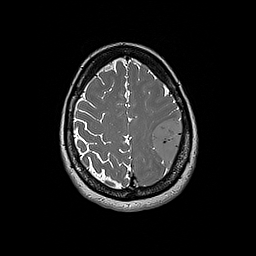
Brain MRI from a brain-tumour surgery series, one axial slice; 1 mm slice thickness; 256 × 256 image matrix. Case-level facts recorded for this patient, not image findings: histopathology: Glioblastoma; WHO grade: 4; IDH mutation: no; tumour location: Left Frontal.
Outlined on this slice (expert manual segmentation):
- tumour: bounding box <152,117,184,165> (left, top, right, bottom; pixels)